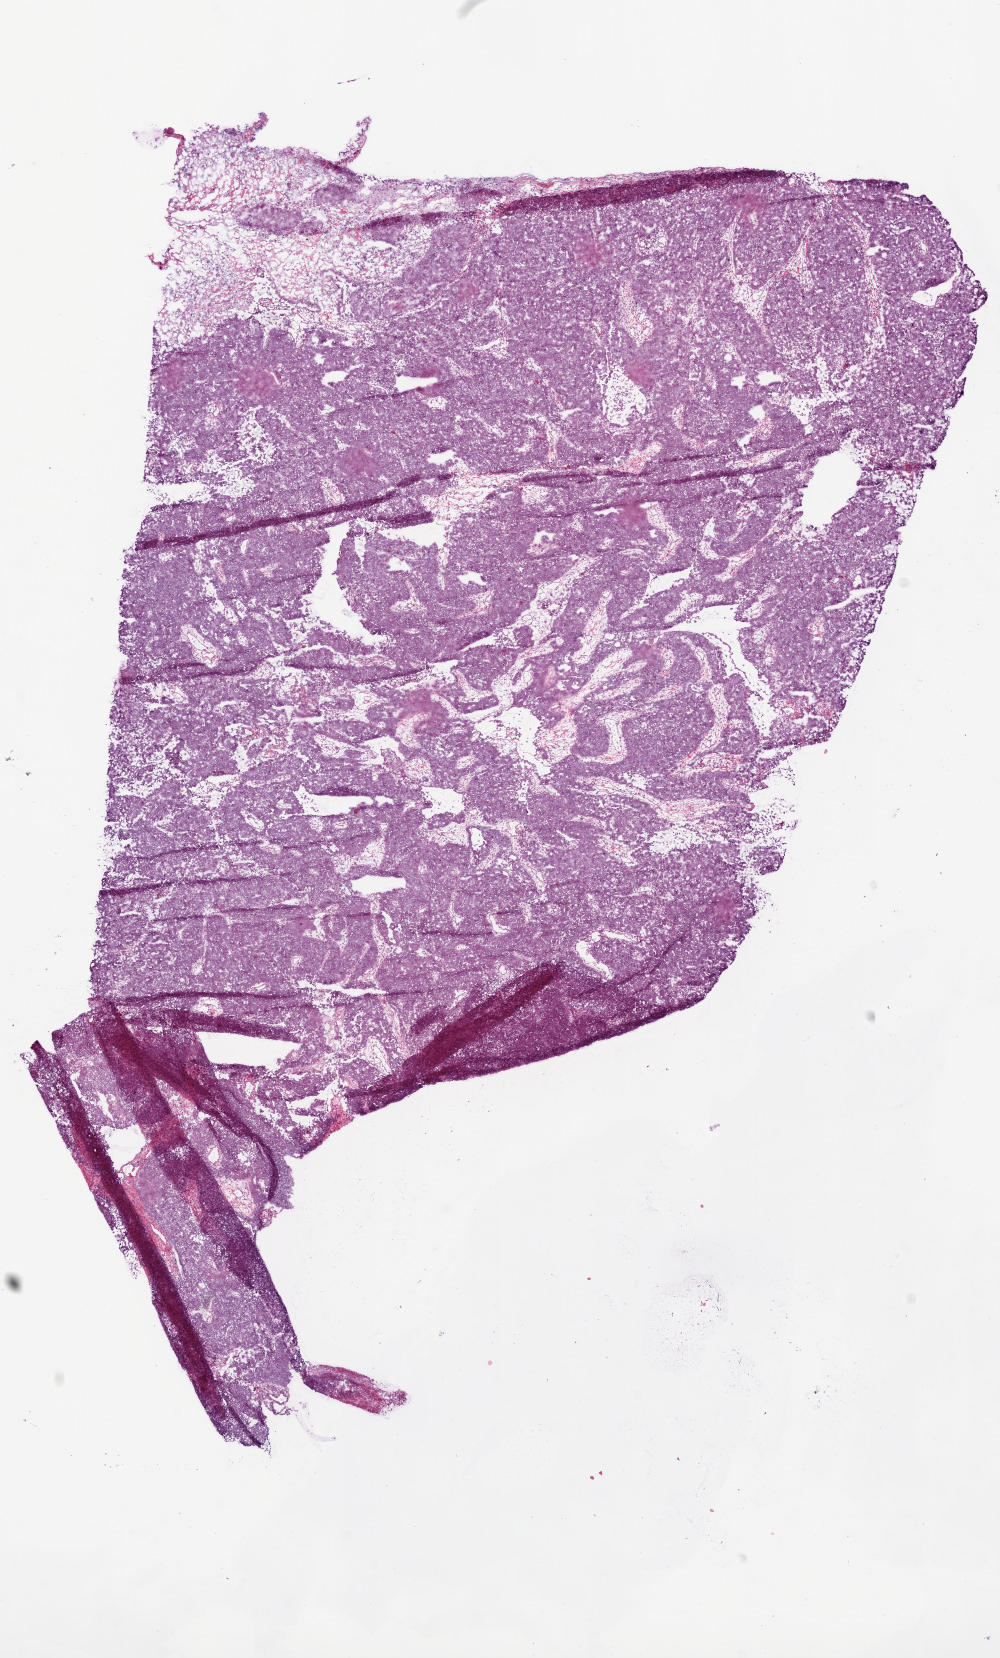
Whole-slide histology image, H&E — whole scanned area (about 8.0 x 13.3 mm, acquisition: 20x scan) shown as a low-resolution overview. Frozen section from the top of the tissue portion. Primary tumour sample from the ovary. Female patient; age at initial diagnosis 60 years. Slide review estimates, as recorded: tumour cells 90%, tumour nuclei 90%.
Pathologic diagnosis: Serous cystadenocarcinoma, NOS.